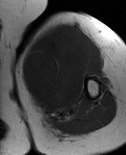
MRI of an extremity soft-tissue mass, one axial slice. MR volume resampled by the dataset authors to the PET/CT grid (not the native acquisition matrix). 3.27 mm slice thickness. 126 × 155 image matrix. Female patient. From the clinical record (not read from this slice): histological type: pleiomorphic leiomyosarcoma; grade: high; site of the primary tumour: left biceps.
Annotated regions visible in this slice (expert contour drawn on MRI and transferred to this co-registered scan by the dataset authors):
- gross tumour volume including surrounding oedema: bounding box [x1, y1, x2, y2] px = [22, 24, 96, 119]
- gross tumour volume (mass): [22, 24, 92, 112]